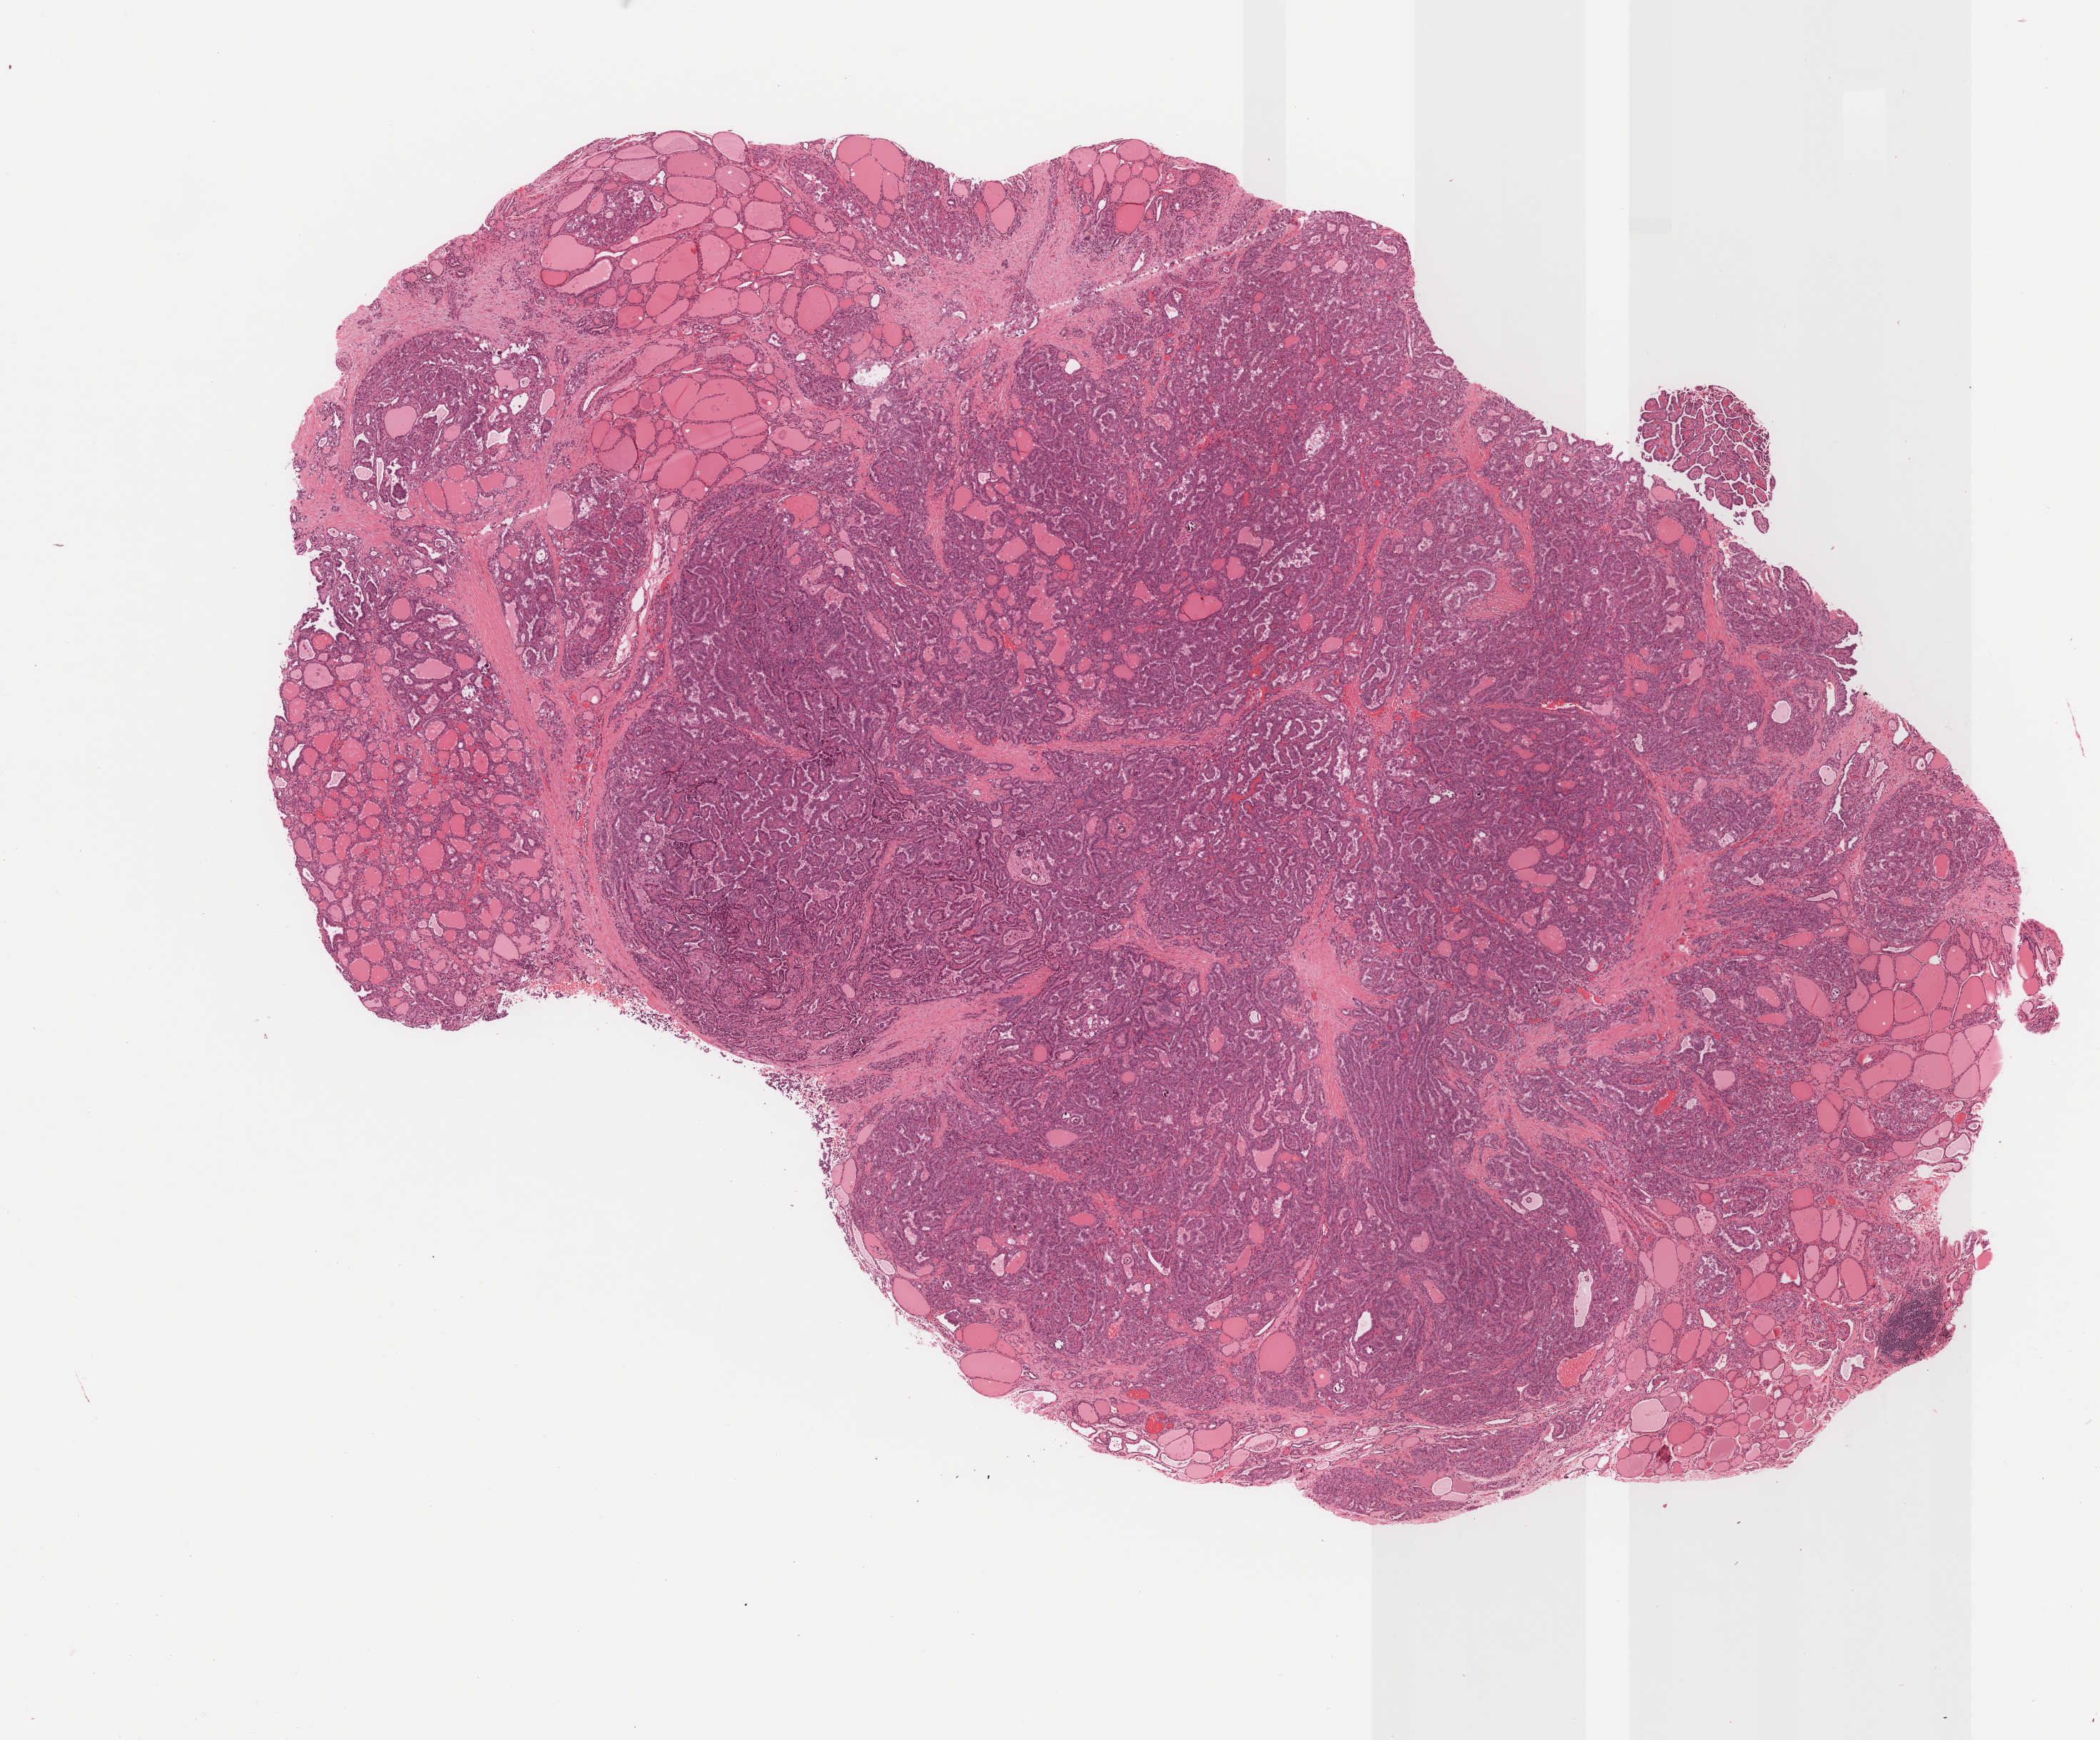
H&E-stained whole-slide image — low-resolution overview of the scanned area, about 11.9 x 9.8 mm (from a 40x scan), formalin-fixed paraffin-embedded (FFPE) diagnostic section, thyroid, primary tumour sample. Female, age 51 years at initial diagnosis.
TNM: T3 N1b MX. Laterality: right. Histologic diagnosis: Papillary carcinoma, oxyphilic cell (thyroid gland). AJCC pathologic stage: IVA (7th edition).